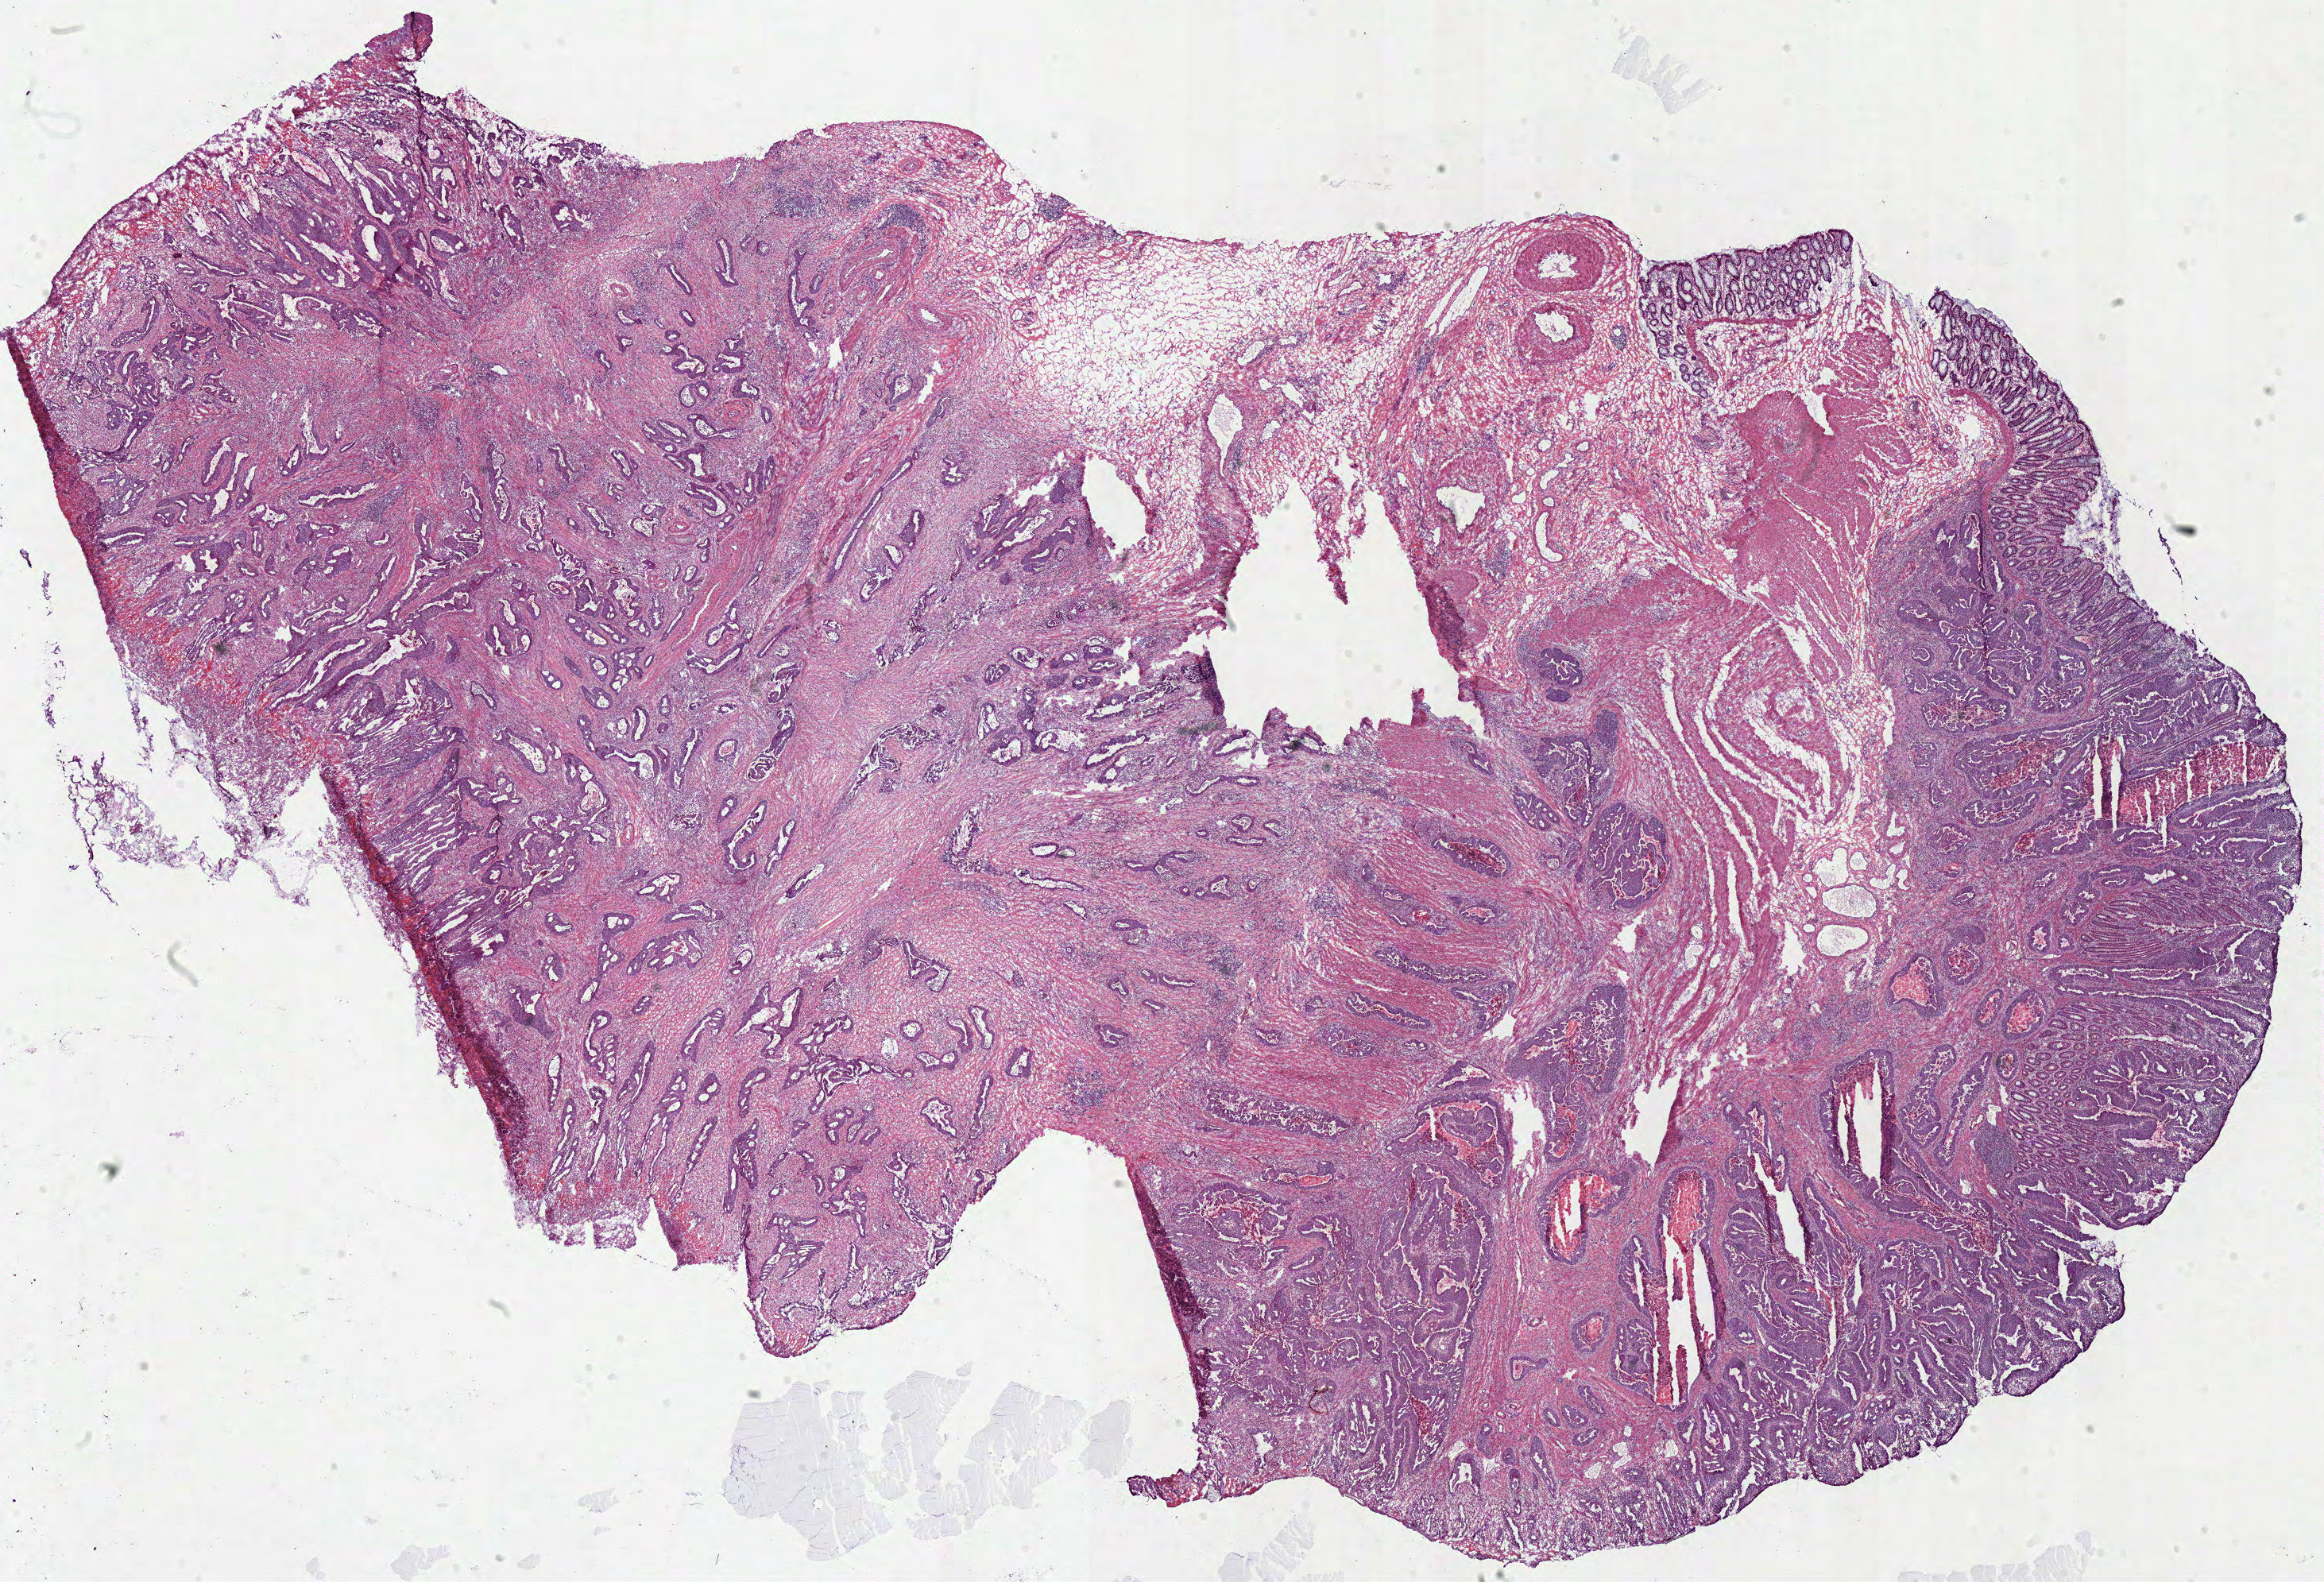
Digitized H&E-stained tissue section (whole slide), whole scanned area (about 23.0 x 15.7 mm, acquisition: 40x scan) shown as a low-resolution overview. Frozen section from the top of the tissue portion. Primary tumour sample from the colon. Male, age 60 years at initial diagnosis. Slide review estimates, as recorded: tumour cells 47%, tumour nuclei 65%, normal cells 8%, stromal cells 30%, necrosis 15%.
- diagnosis: Adenocarcinoma, NOS
- TNM: T2 N0 M0
- AJCC pathologic stage: I (7th edition)